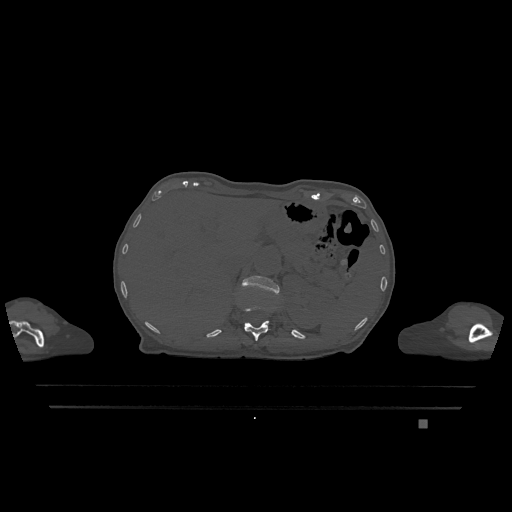
CT including the spine, one axial slice; slice 518 of 1317 in the series (ordered by position); bone window (W 1800 / L 400 HU); 0.5 mm slice thickness; 512 × 512 image matrix, field of view 500 × 500 mm. Patient: female, 74 years. Case-level facts recorded for this patient, not image findings: primary cancer: lung.
Outlined on this slice (semi-automatically segmented with operator editing):
- L1 vertebra: bounding box (x1, y1, x2, y2) in pixels: (242, 275, 279, 295)
- T12 vertebra: (244, 305, 269, 341)